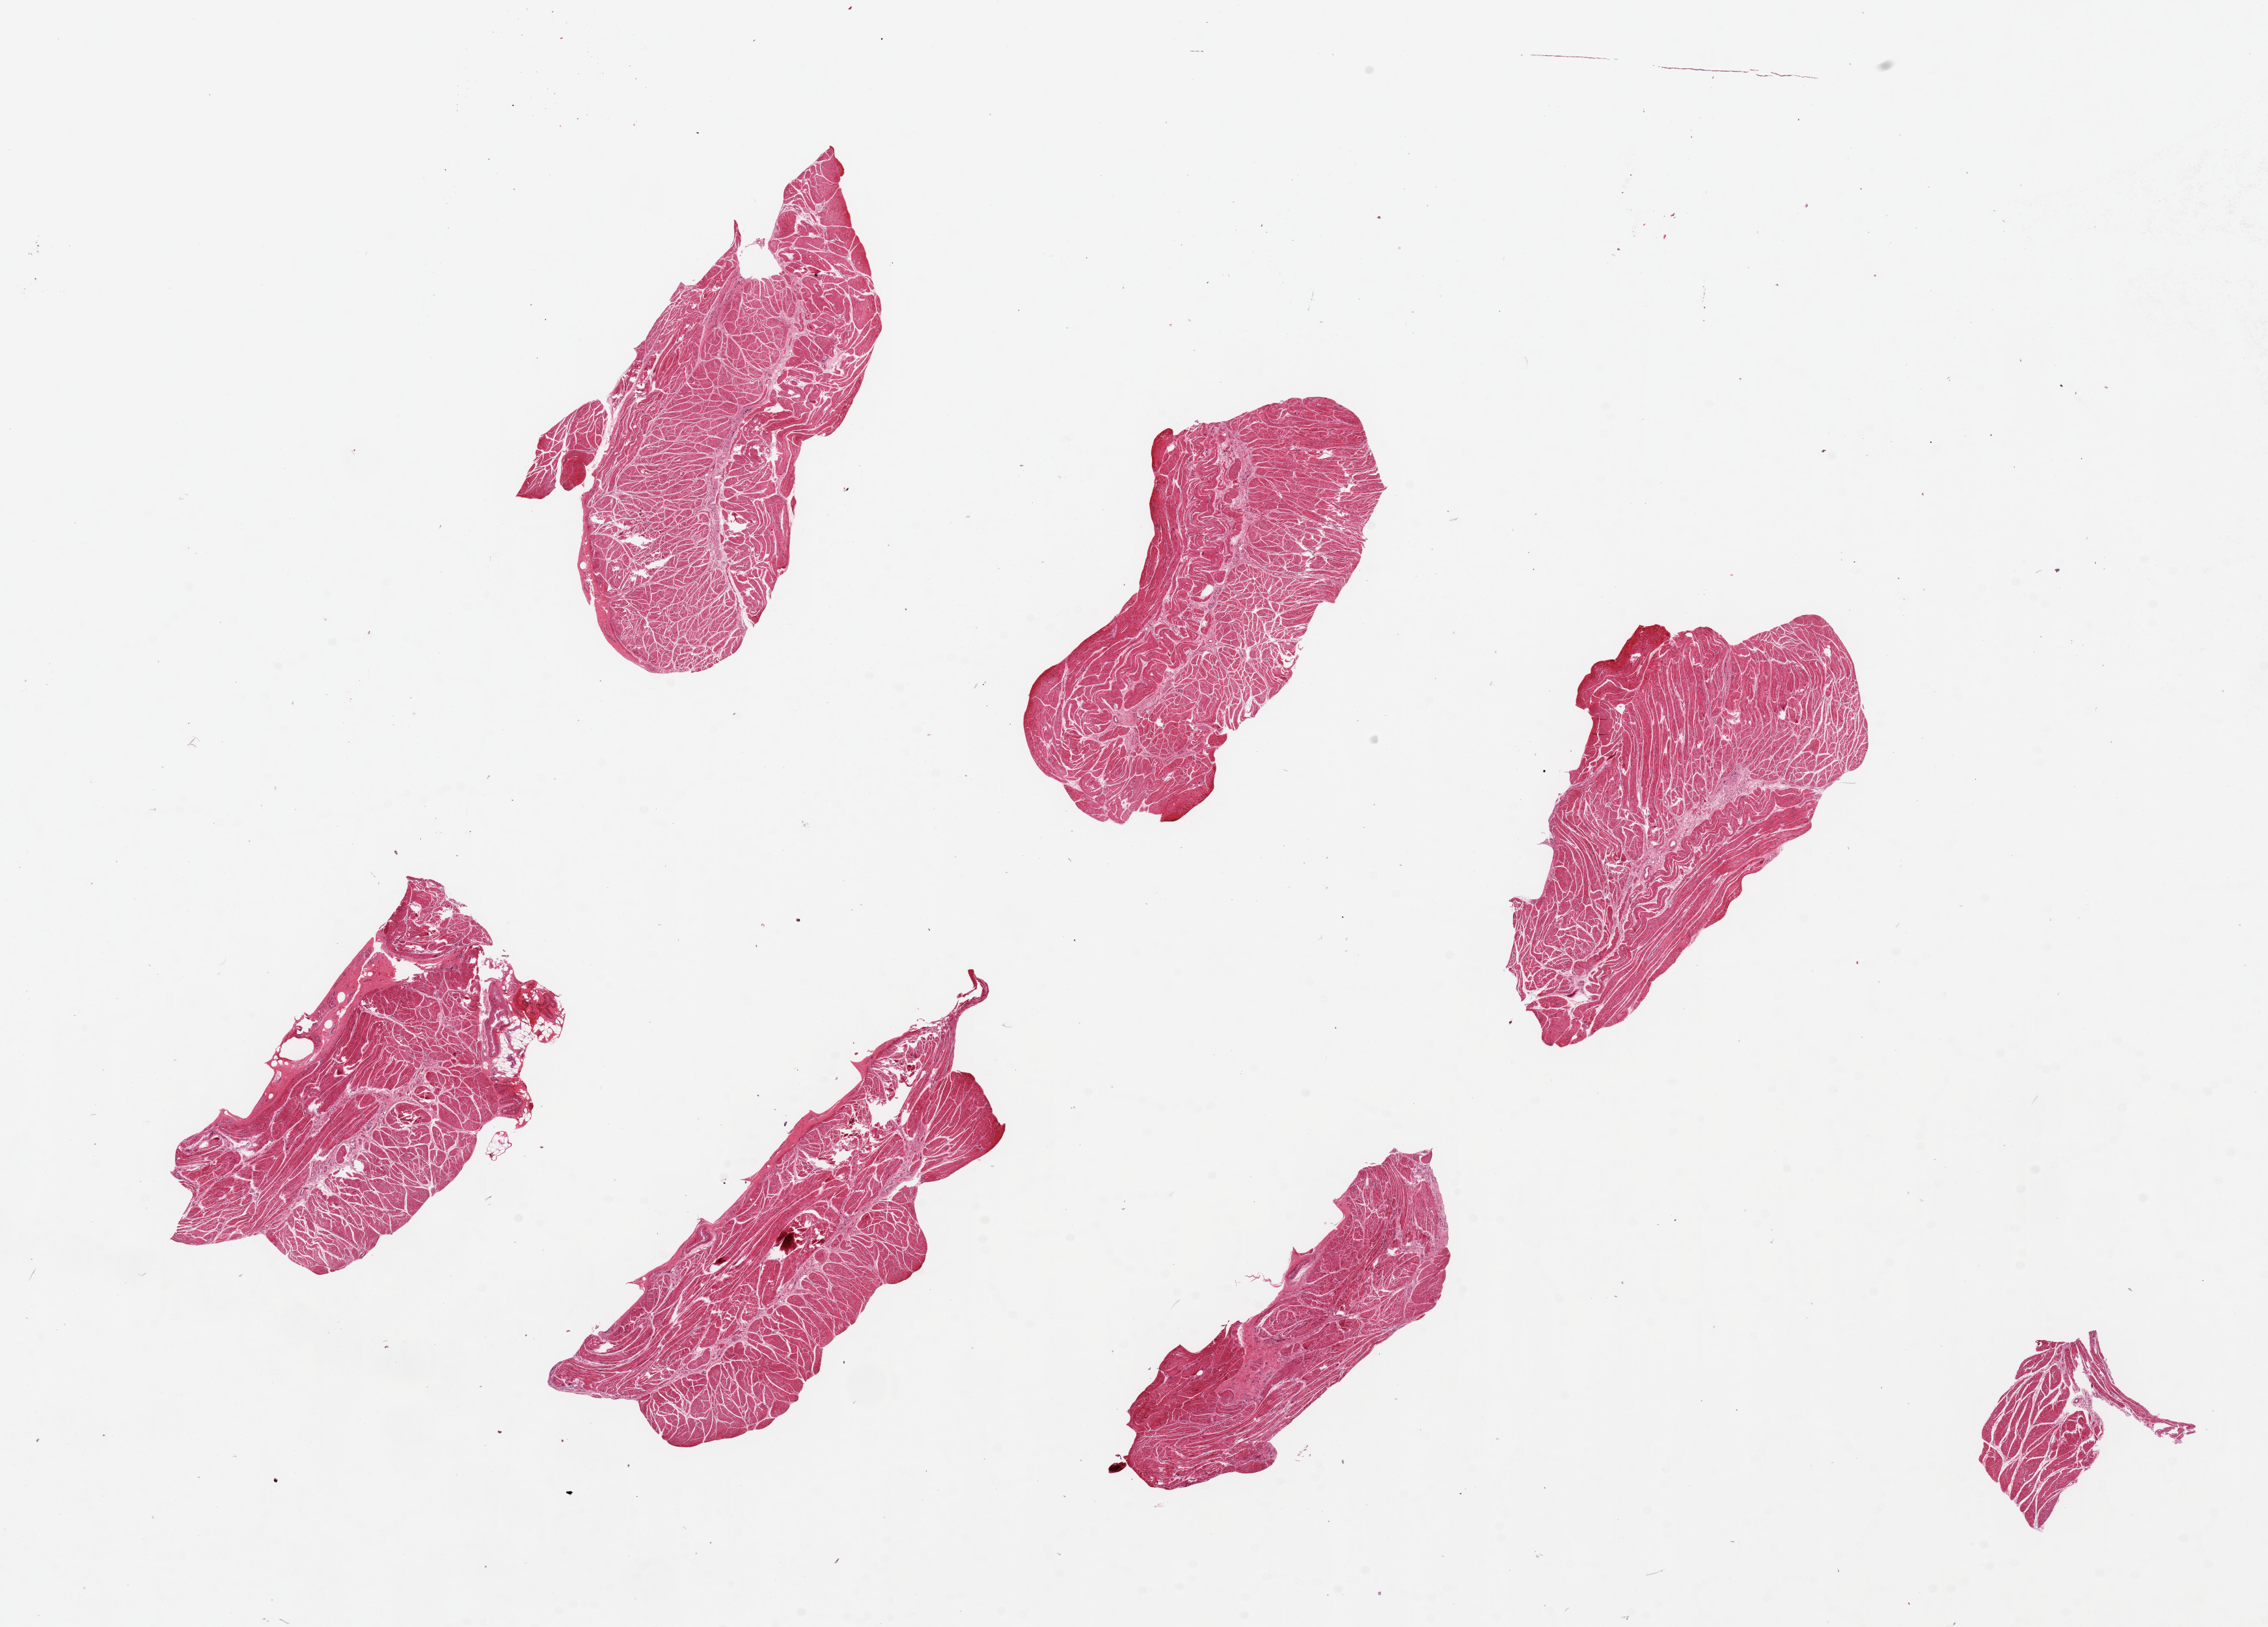
Whole-slide image, hematoxylin and eosin (H&E) stain, brightfield, low-resolution overview of the scanned area, about 27.6 x 19.8 mm, PAXgene-fixed, paraffin-embedded tissue, sampled site (target tissue): gastroesophageal junction, tissue donor sample. Donor sex: male.
Pathologist's review note for this sample: 6 pieces ~6x3mm, all muscle, clean specimens.